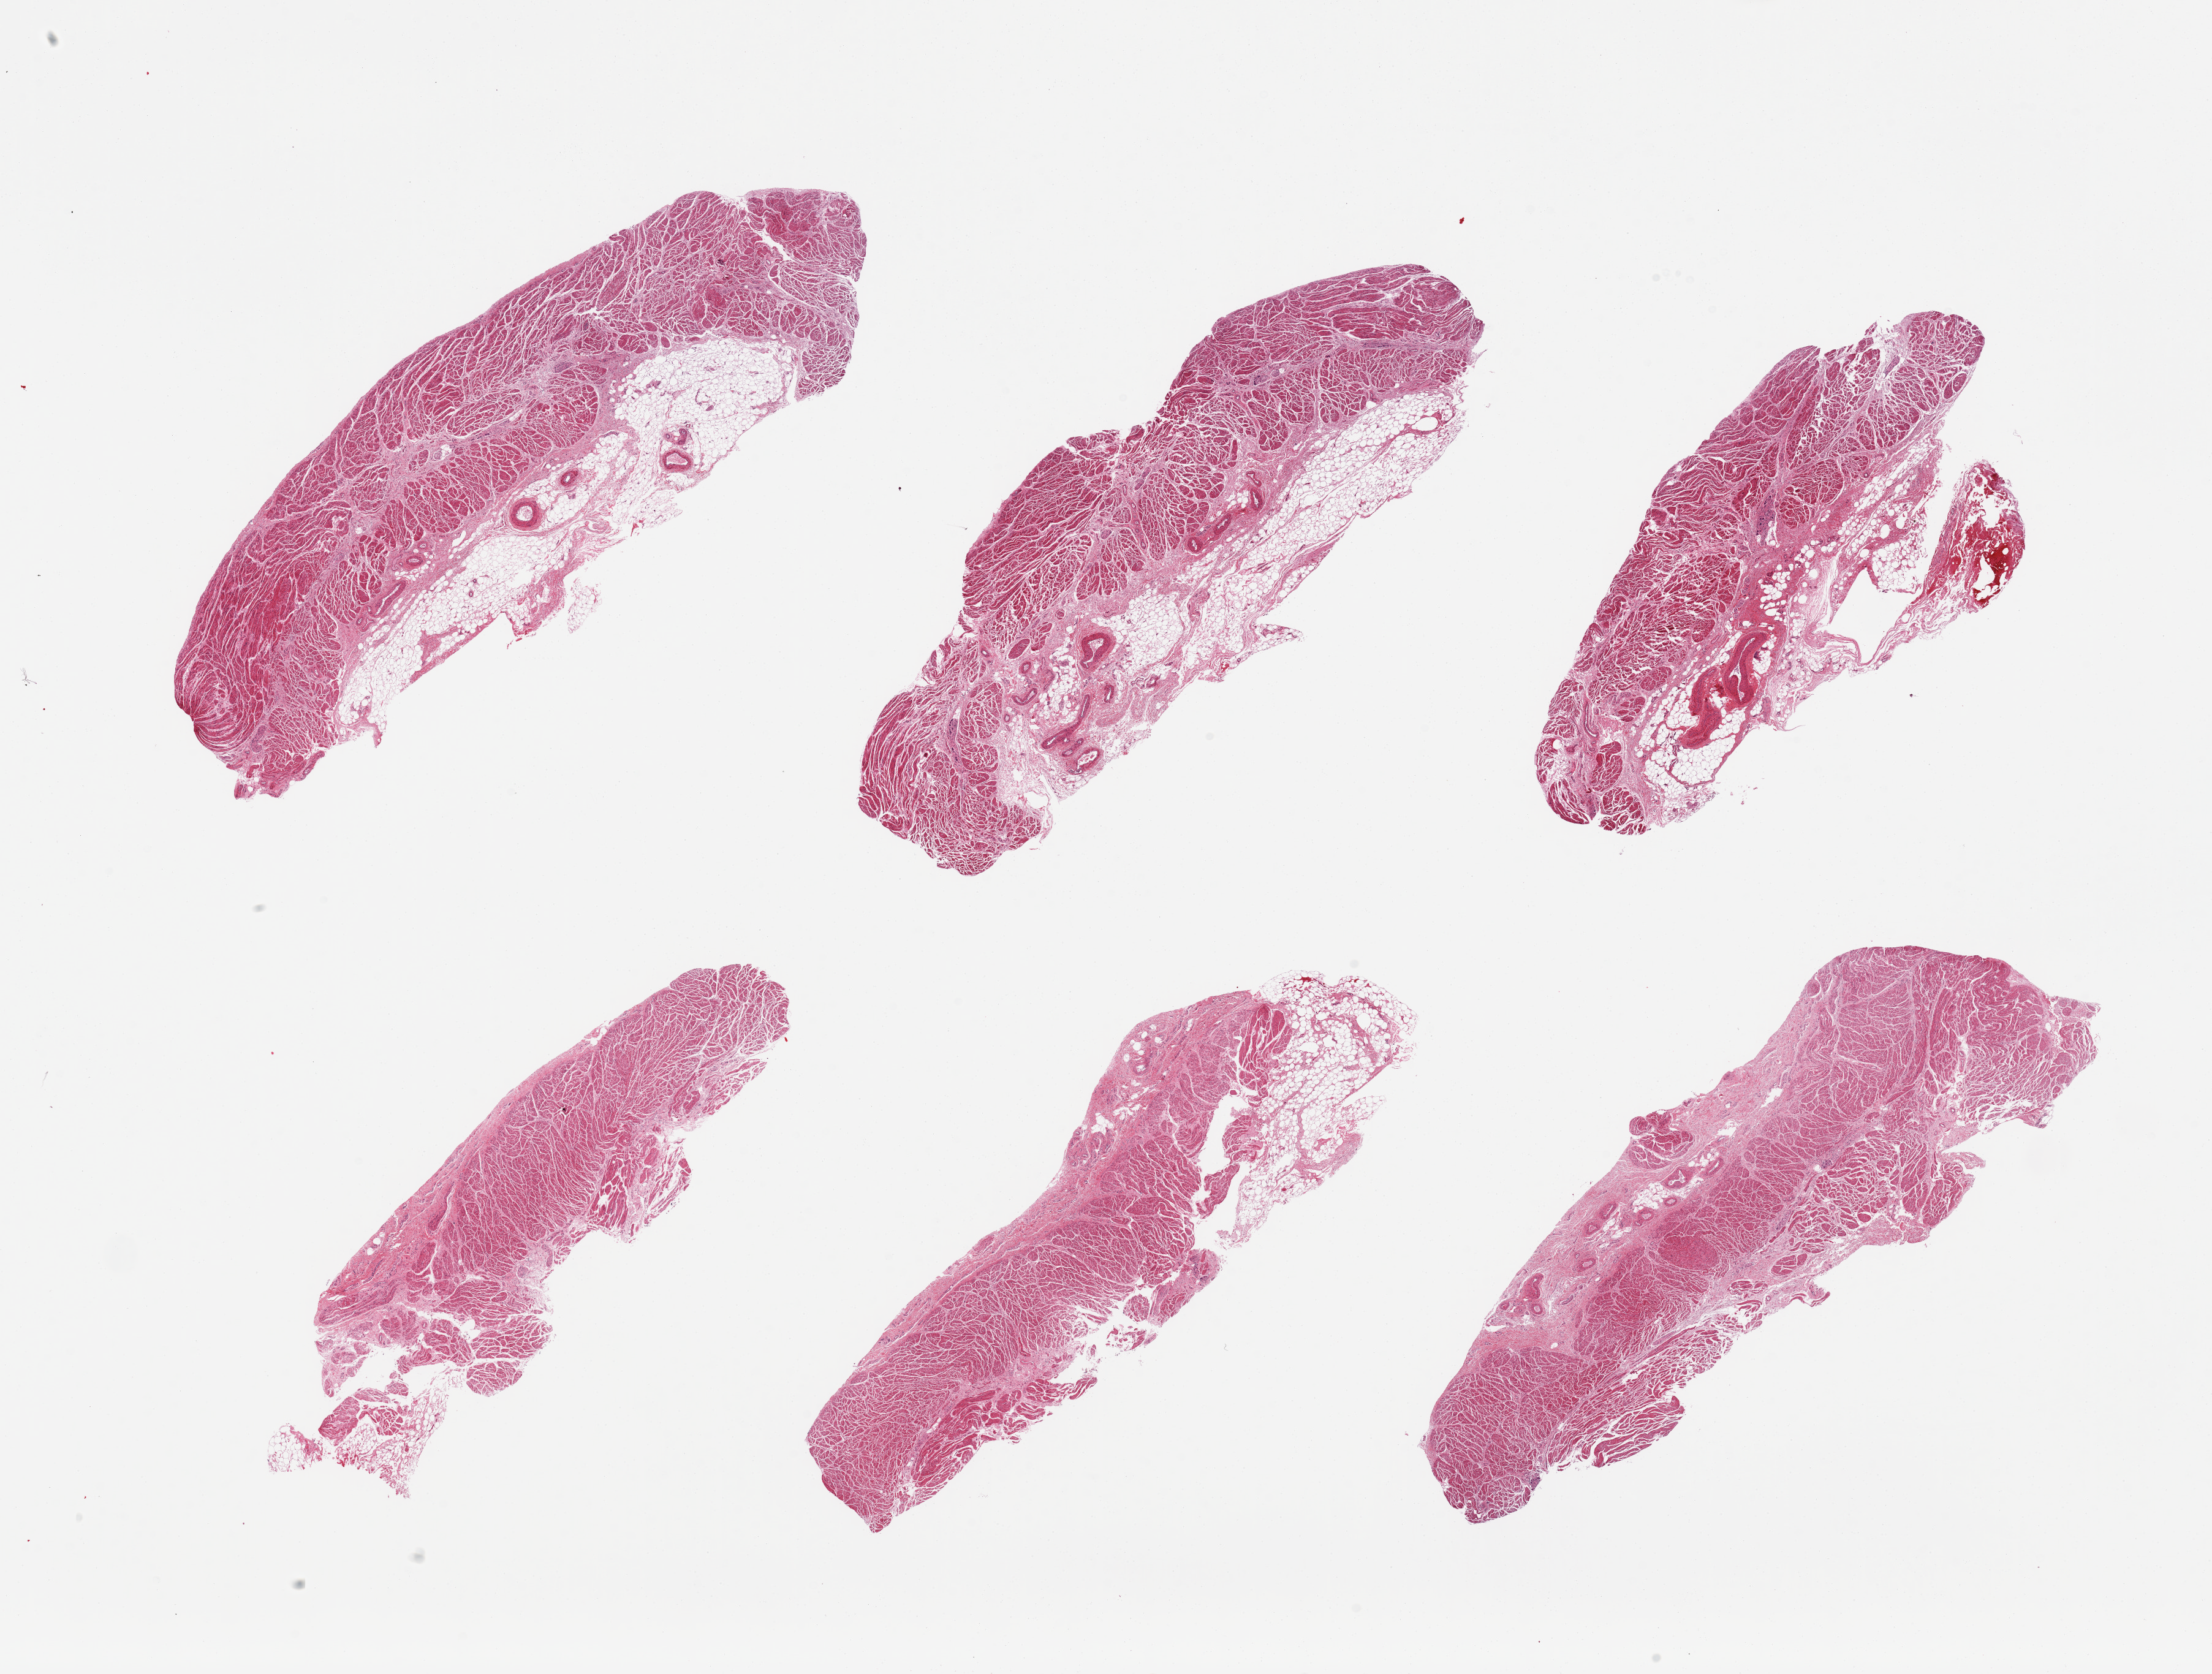
Whole-slide image, hematoxylin and eosin (H&E) stain, brightfield — a low-resolution overview of the entire scanned area, about 28.5 x 21.6 mm. PAXgene-fixed, paraffin-embedded tissue. Section of gastroesophageal junction (target tissue). Tissue donor sample. Male donor.
Pathologist's review note for this sample: 6 pieces, muscularis and attached adipose tissue/vessels.